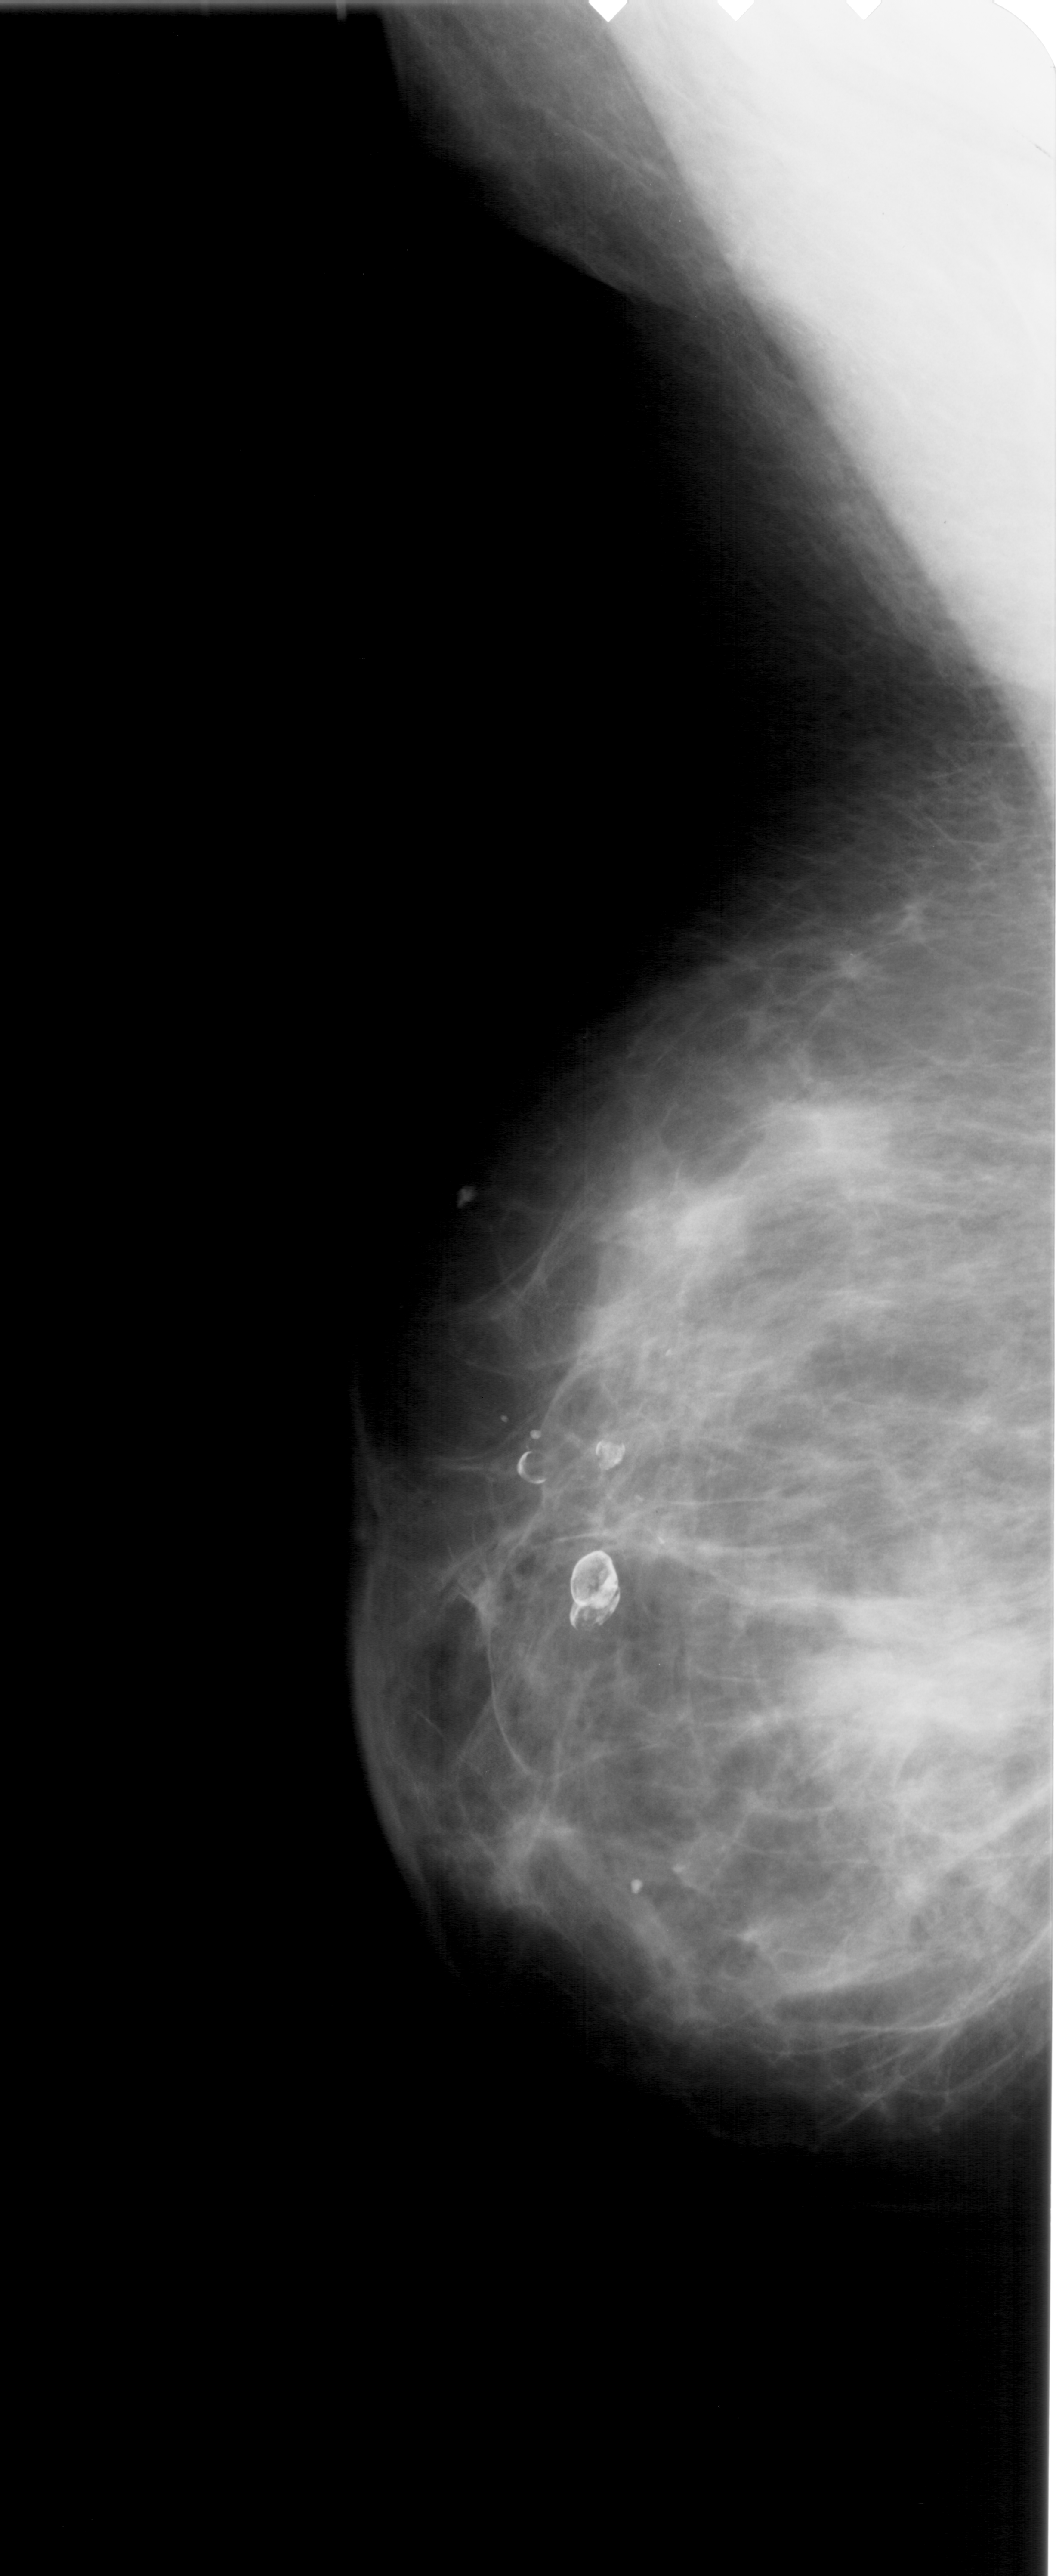
Digitized screen-film mammogram; left breast; mediolateral oblique (MLO) view; breast composition: scattered fibroglandular densities (BI-RADS density category 2 of 4); 1059 × 2576 image matrix.
Marked abnormalities (boxes around the expert regions of interest):
- mass, shape irregular, margins ill defined; BI-RADS assessment category 5; subtlety rating 5 on a 1 (subtle) to 5 (obvious) scale; pathology (as recorded): malignant: box from (x=821, y=1573) to (x=1038, y=1844) px